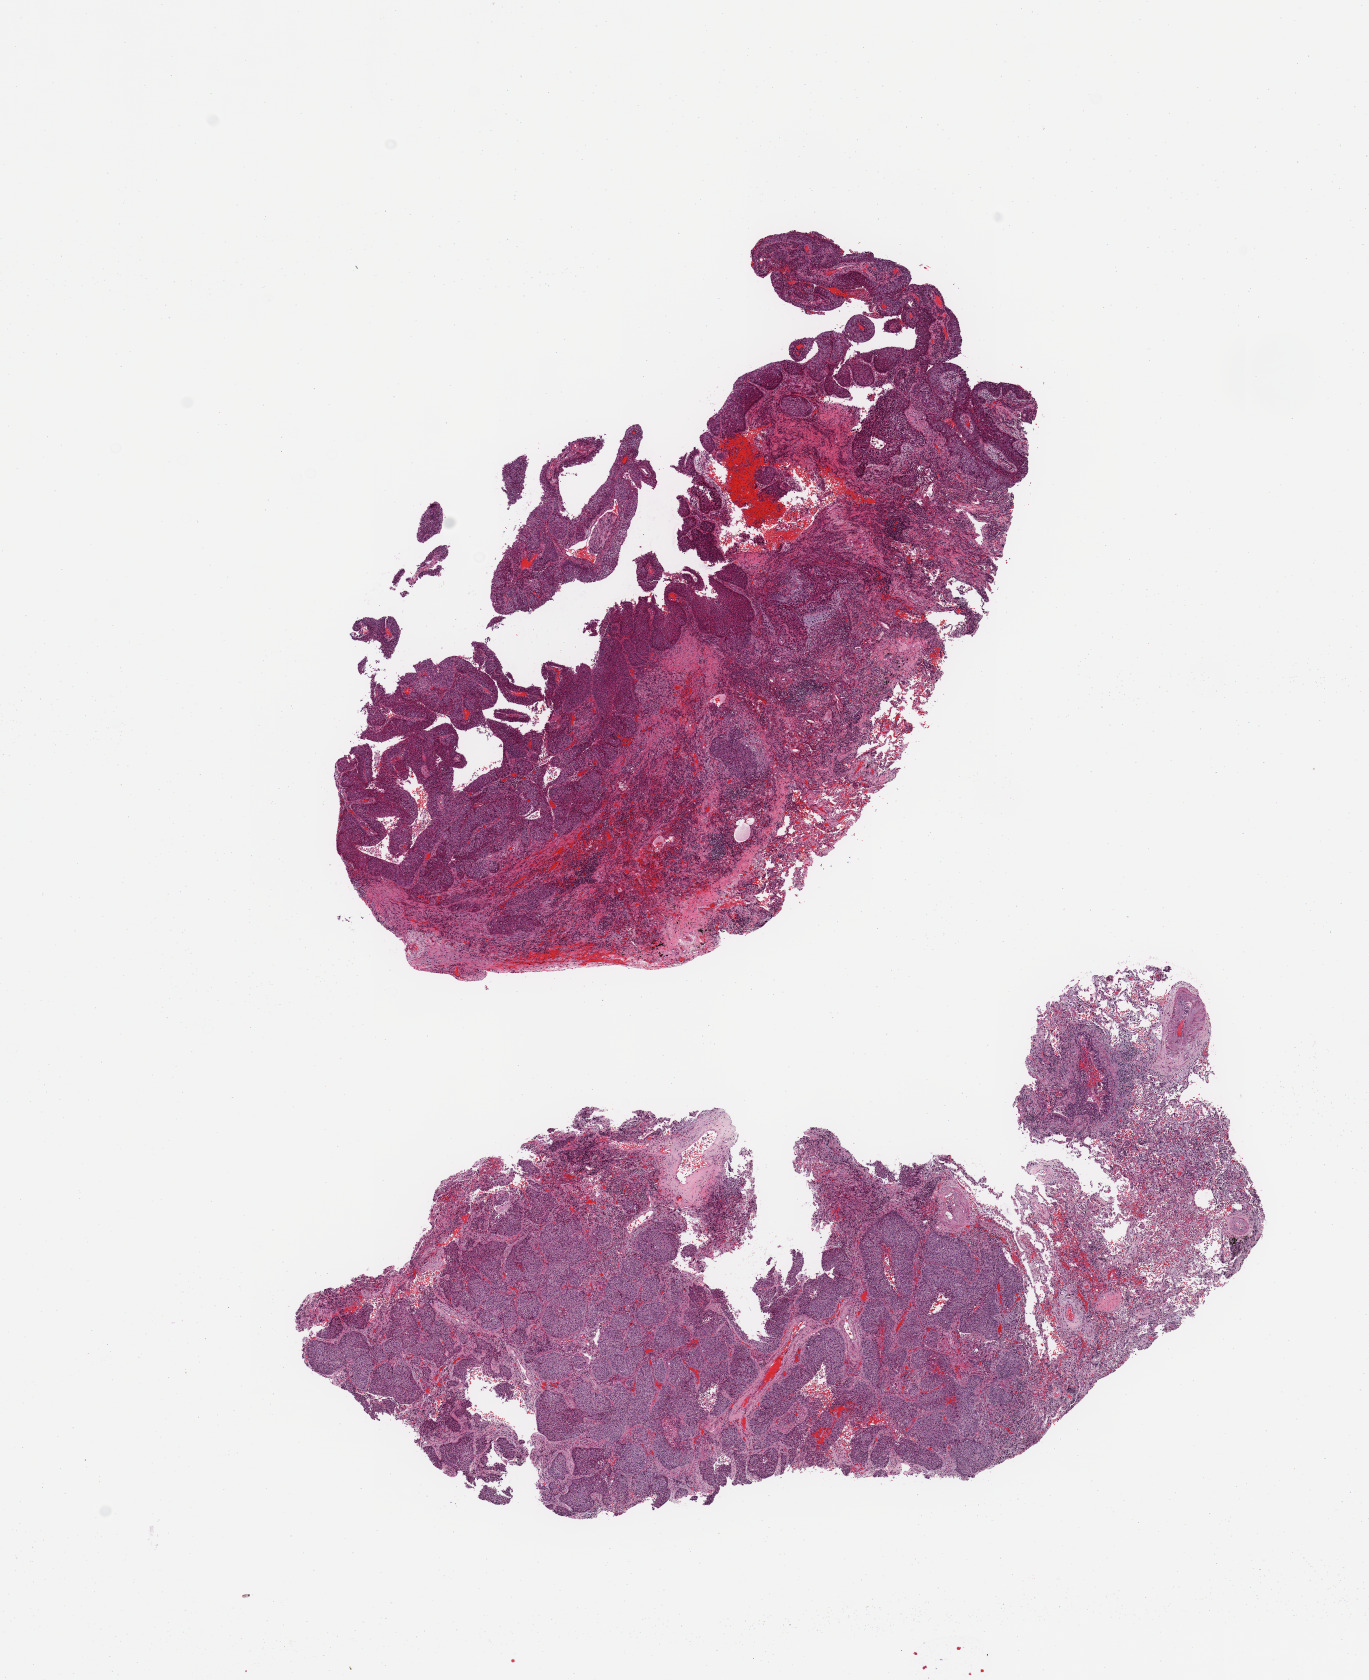
H&E-stained whole-slide image, low-resolution overview of the scanned area, about 10.8 x 13.3 mm, tumour tissue sample, sampled site: lung. Patient: male, age 66 years. Histologic grade: G2 (moderately differentiated). Pathologist review of this section (percent, as recorded): tumour nuclei 85%, necrosis 5%.
Primary tumour site (as recorded): right upper lobe. Diagnosis: Squamous cell carcinoma, NOS. AJCC pathologic stage: IB.